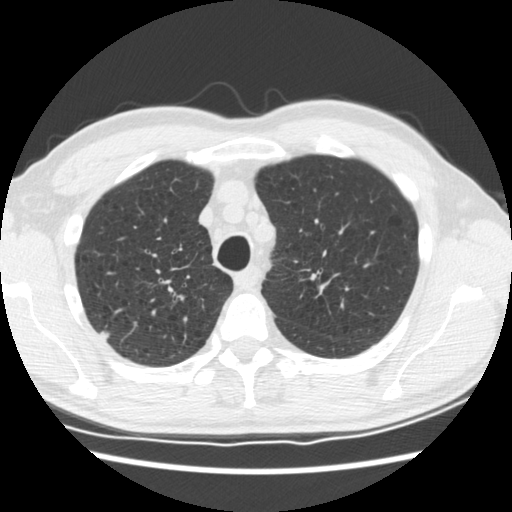
Low-dose screening chest CT, one axial slice. Slice 142 of 183 in the series (ordered by position). Reconstruction kernel STANDARD. 120 kVp. Lung window (W 1500 / L -600 HU). 512 × 512 image matrix, field of view 339 × 339 mm.
Outlined on this slice (manually delineated by an expert):
- lesion 2 (tumor, upper lobe of right lung): bounding box <100,330,111,340> (left, top, right, bottom; pixels)